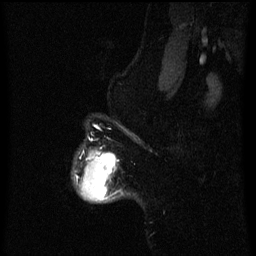
Breast MRI (dynamic contrast-enhanced), one sagittal slice. Slice 56 of 60 in the series (ordered by position). Dynamic contrast-enhanced series, image 2 of 3 at this slice position (ordered by acquisition). 1.5 T. TE 4.2 ms, TR 8 ms. 2 mm slice thickness. 256 × 256 image matrix. Patient: female, 50 years.
Outlined on this slice (semi-automatically segmented with operator editing):
- analysis volume of interest (the breast-tissue region the enhancement analysis was run in; not a lesion): bounding box <73,150,118,203> (left, top, right, bottom; pixels)
- tumour enhancement mask (voxels above the 70 % enhancement threshold inside the analysis volume of interest): <75,151,116,200>